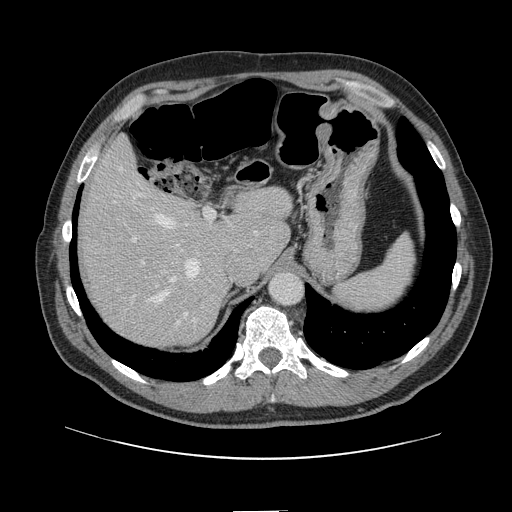
Contrast-enhanced abdominal CT, one axial slice; slice 101 of 161 in the series (ordered by position); intravenous contrast given; soft-tissue window (W 400 / L 40 HU); 2.5 mm slice thickness; 512 × 512 image matrix, field of view 412 × 412 mm. Male patient, age 66 years. From the clinical record (not read from this slice): diagnosis: colorectal cancer liver metastases, imaged before liver resection; multiple liver metastases: no; largest metastasis: 3.5 cm.
Structures marked on this image (outlined manually by an expert reader):
- hepatic veins: bounding box (x1, y1, x2, y2) in pixels: (115, 168, 200, 305)
- liver: (82, 142, 291, 347)
- planned liver remnant (the part of the liver to remain after resection): (82, 142, 291, 307)
- portal vein (with intrahepatic branches): (131, 209, 216, 308)